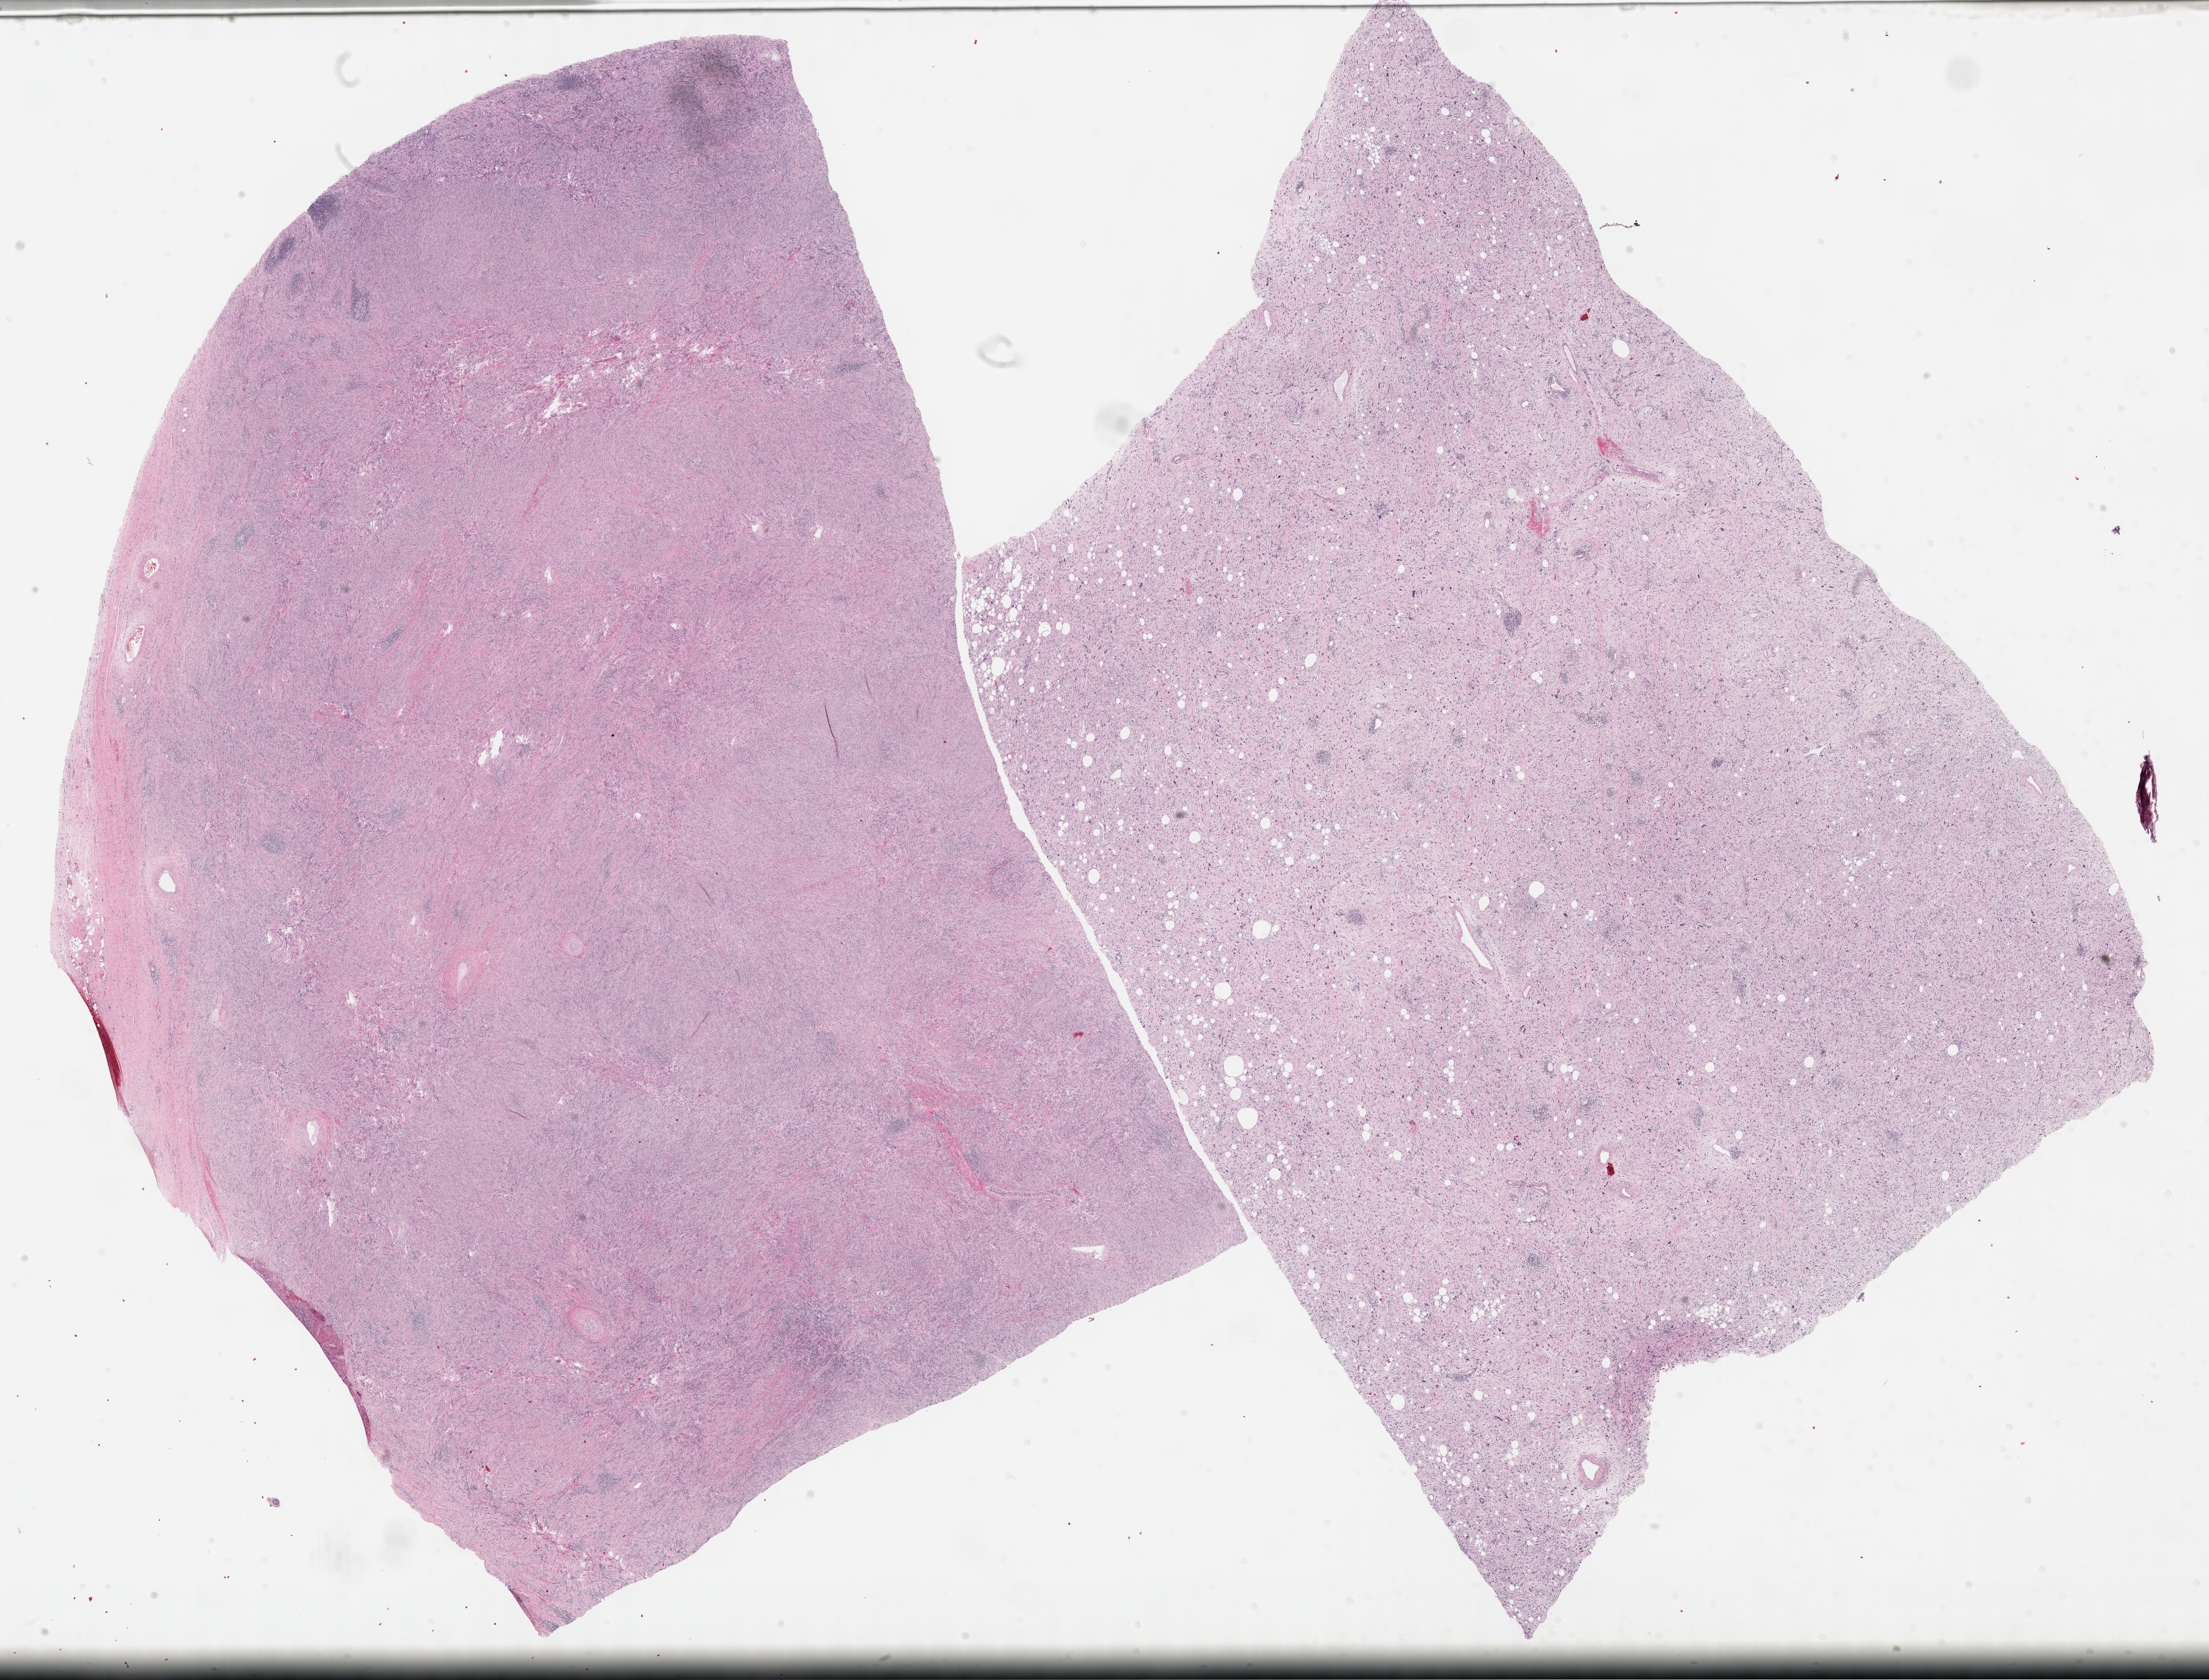
Whole-slide histology image, H&E-stained, low-resolution overview of the scanned area, about 31.2 x 23.7 mm; formalin-fixed paraffin-embedded (FFPE) diagnostic section; retroperitoneum and peritoneum, primary tumour sample. Male, age 36 years at initial diagnosis.
Pathologic diagnosis: Dedifferentiated liposarcoma (retroperitoneum).